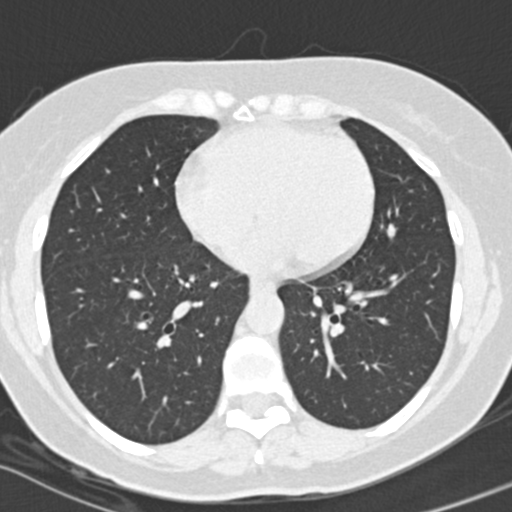
Axial slice from a low-dose chest CT screening exam, baseline screening round, lung window (W 1500 / L -600 HU), 2 mm slice thickness, standard (soft-tissue) reconstruction kernel (B30f), 120 kVp. Female participant, aged 56 years at enrolment. Former smoker at enrolment.
• Expert reader's lesion annotation, bounding box <367,212,408,253> (left, top, right, bottom; pixels).
• Reader record for this screening exam (exam-level; its link to the box is not recorded): non-calcified nodule or mass ≥4 mm, lingula, 7 × 5 mm, smooth margins, soft tissue attenuation.
• Official screen result: positive, change unspecified: nodule(s) >= 4 mm or enlarging nodule(s), mass(es), or other non-specific abnormalities suspicious for lung cancer.